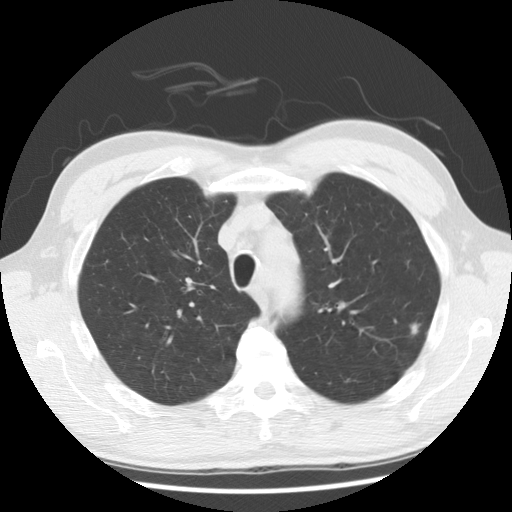
Low-dose screening chest CT, one axial slice. Position 116 of 148 along the scan axis. 140 kVp. Lung window (W 1500 / L -600 HU). 512 × 512 image matrix, field of view 350 × 350 mm.
Outlined on this slice (manually delineated by an expert):
- lesion 1 (tumor, upper lobe of left lung): bounding box <409,322,421,336> (left, top, right, bottom; pixels)